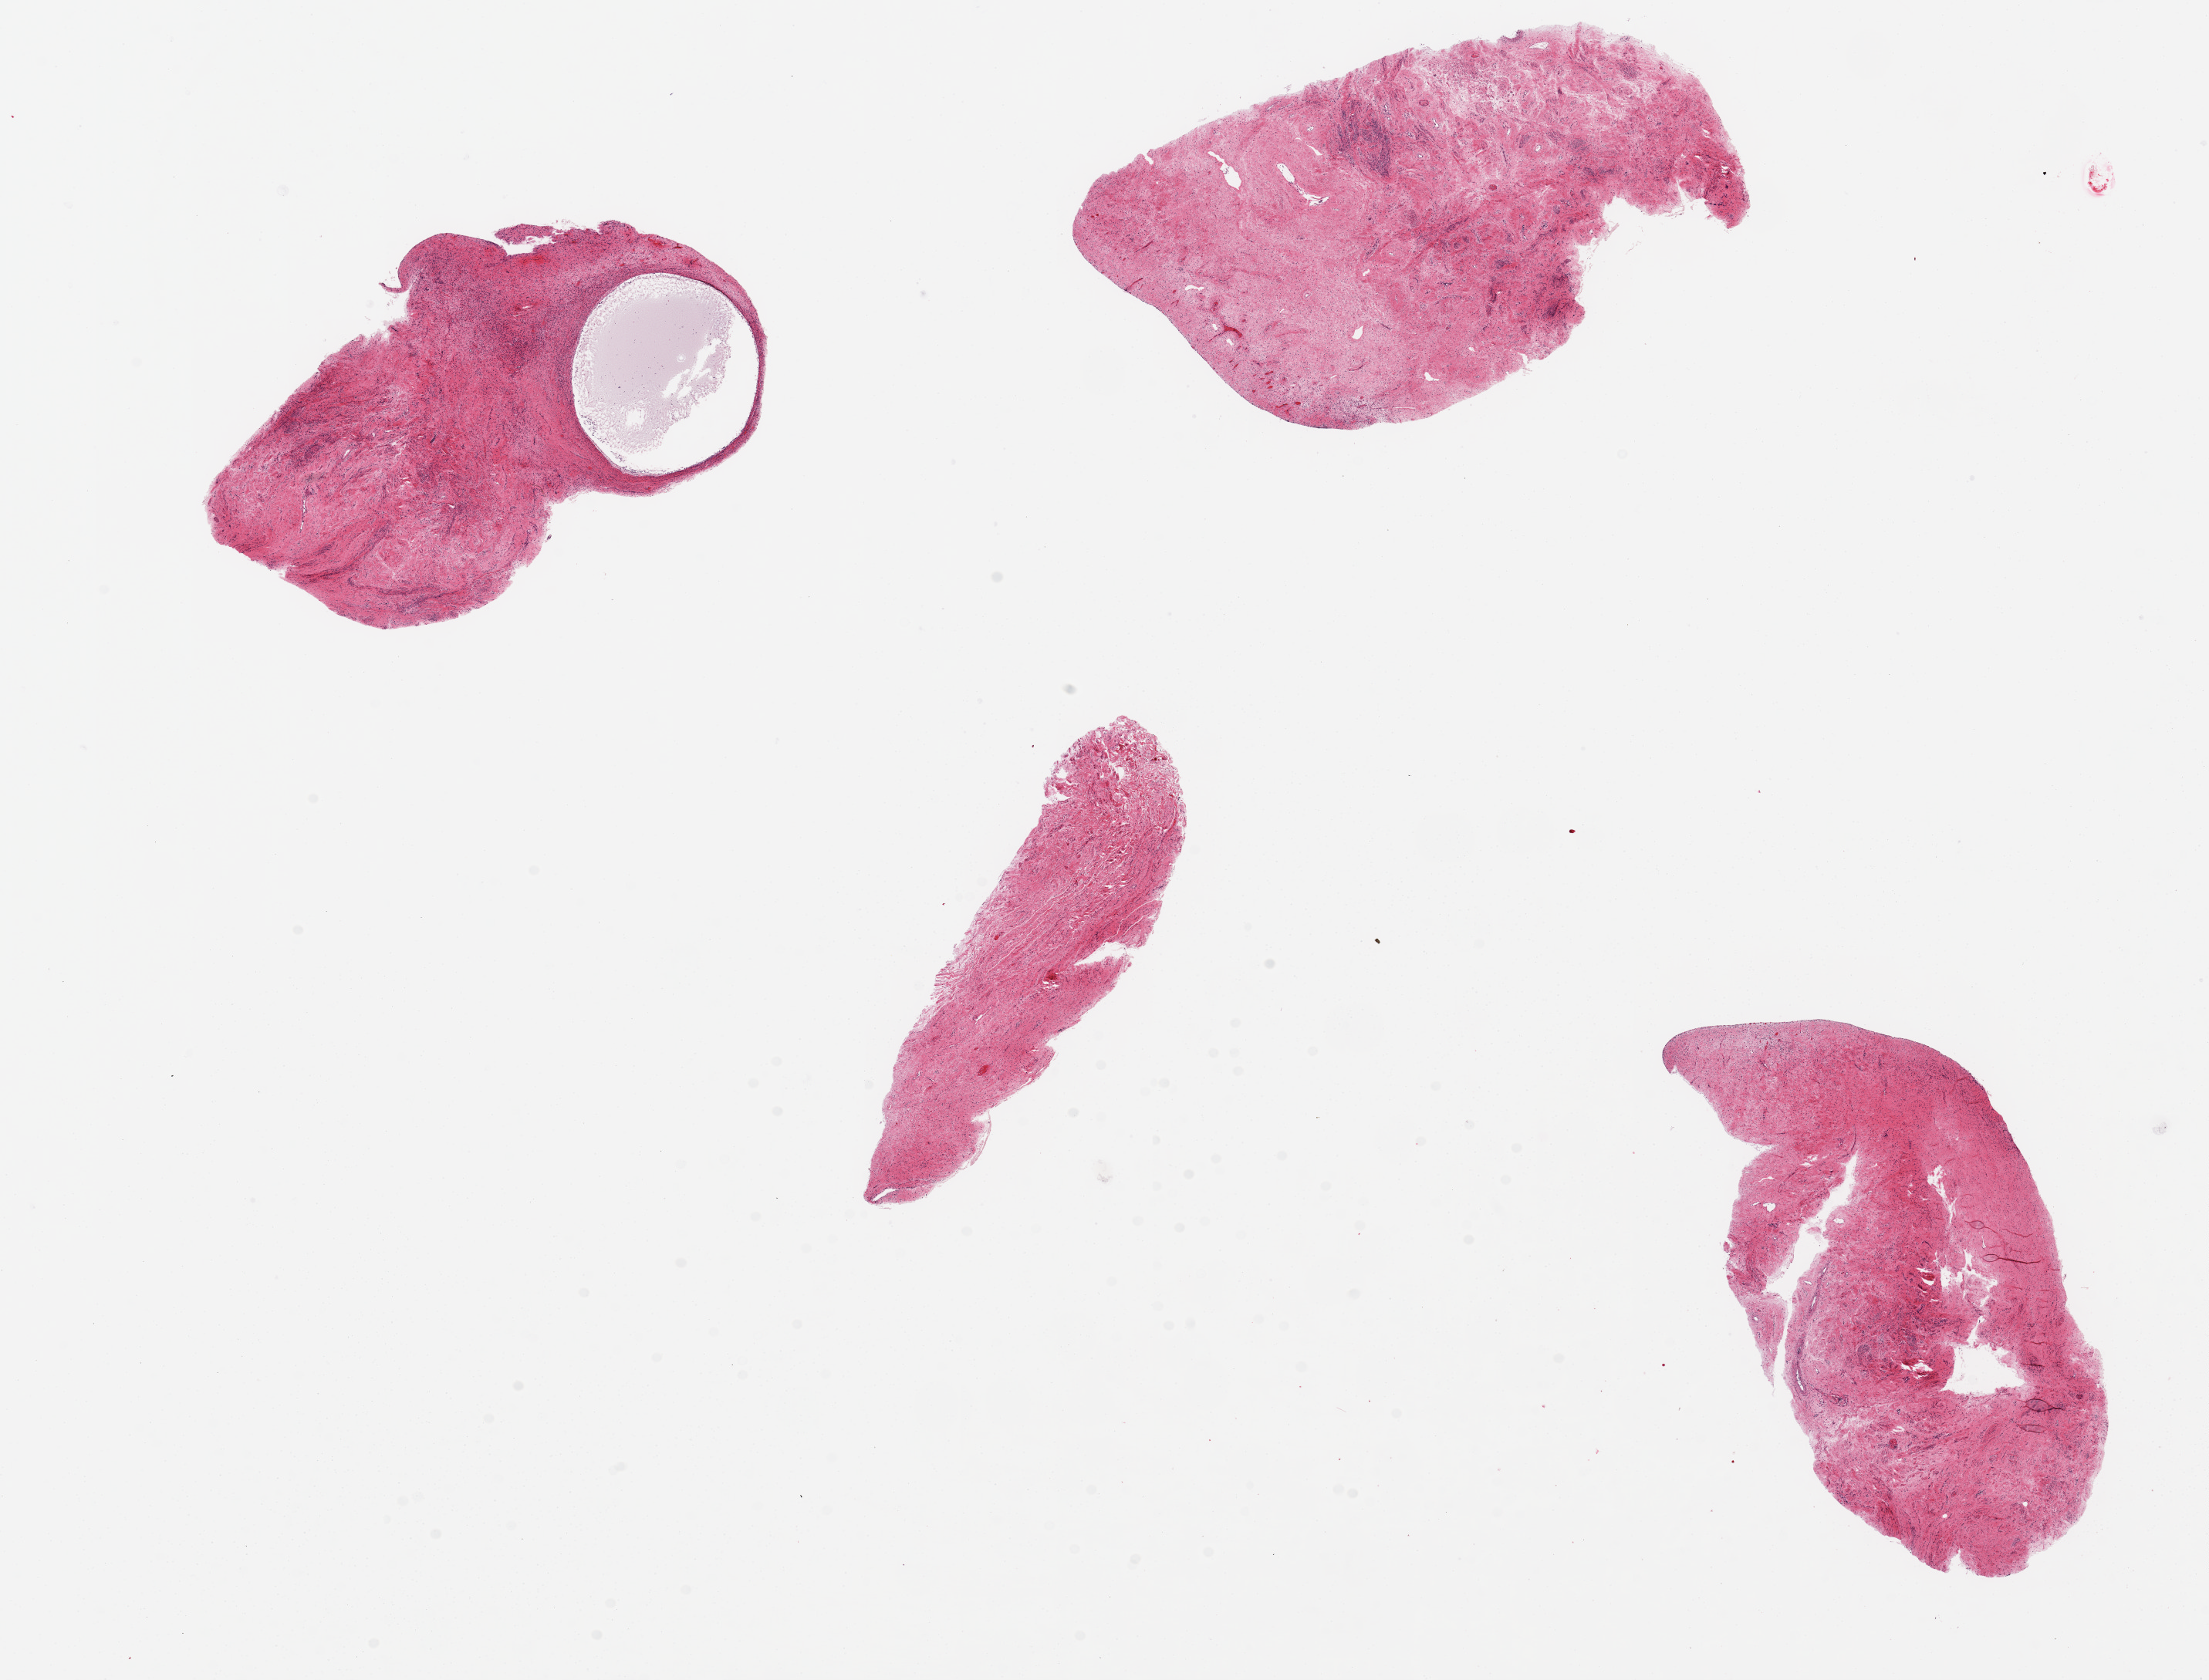
Whole-slide image, haematoxylin and eosin stain, low-resolution overview of the scanned area, about 22.6 x 17.2 mm (slide scanned at 20x). PAXgene-fixed, paraffin-embedded tissue. Sampled site (target tissue): exocervix. Tissue donor sample.
- review note (as recorded): 4 aliquots, ~6x5mm. No visible squamous mucosa